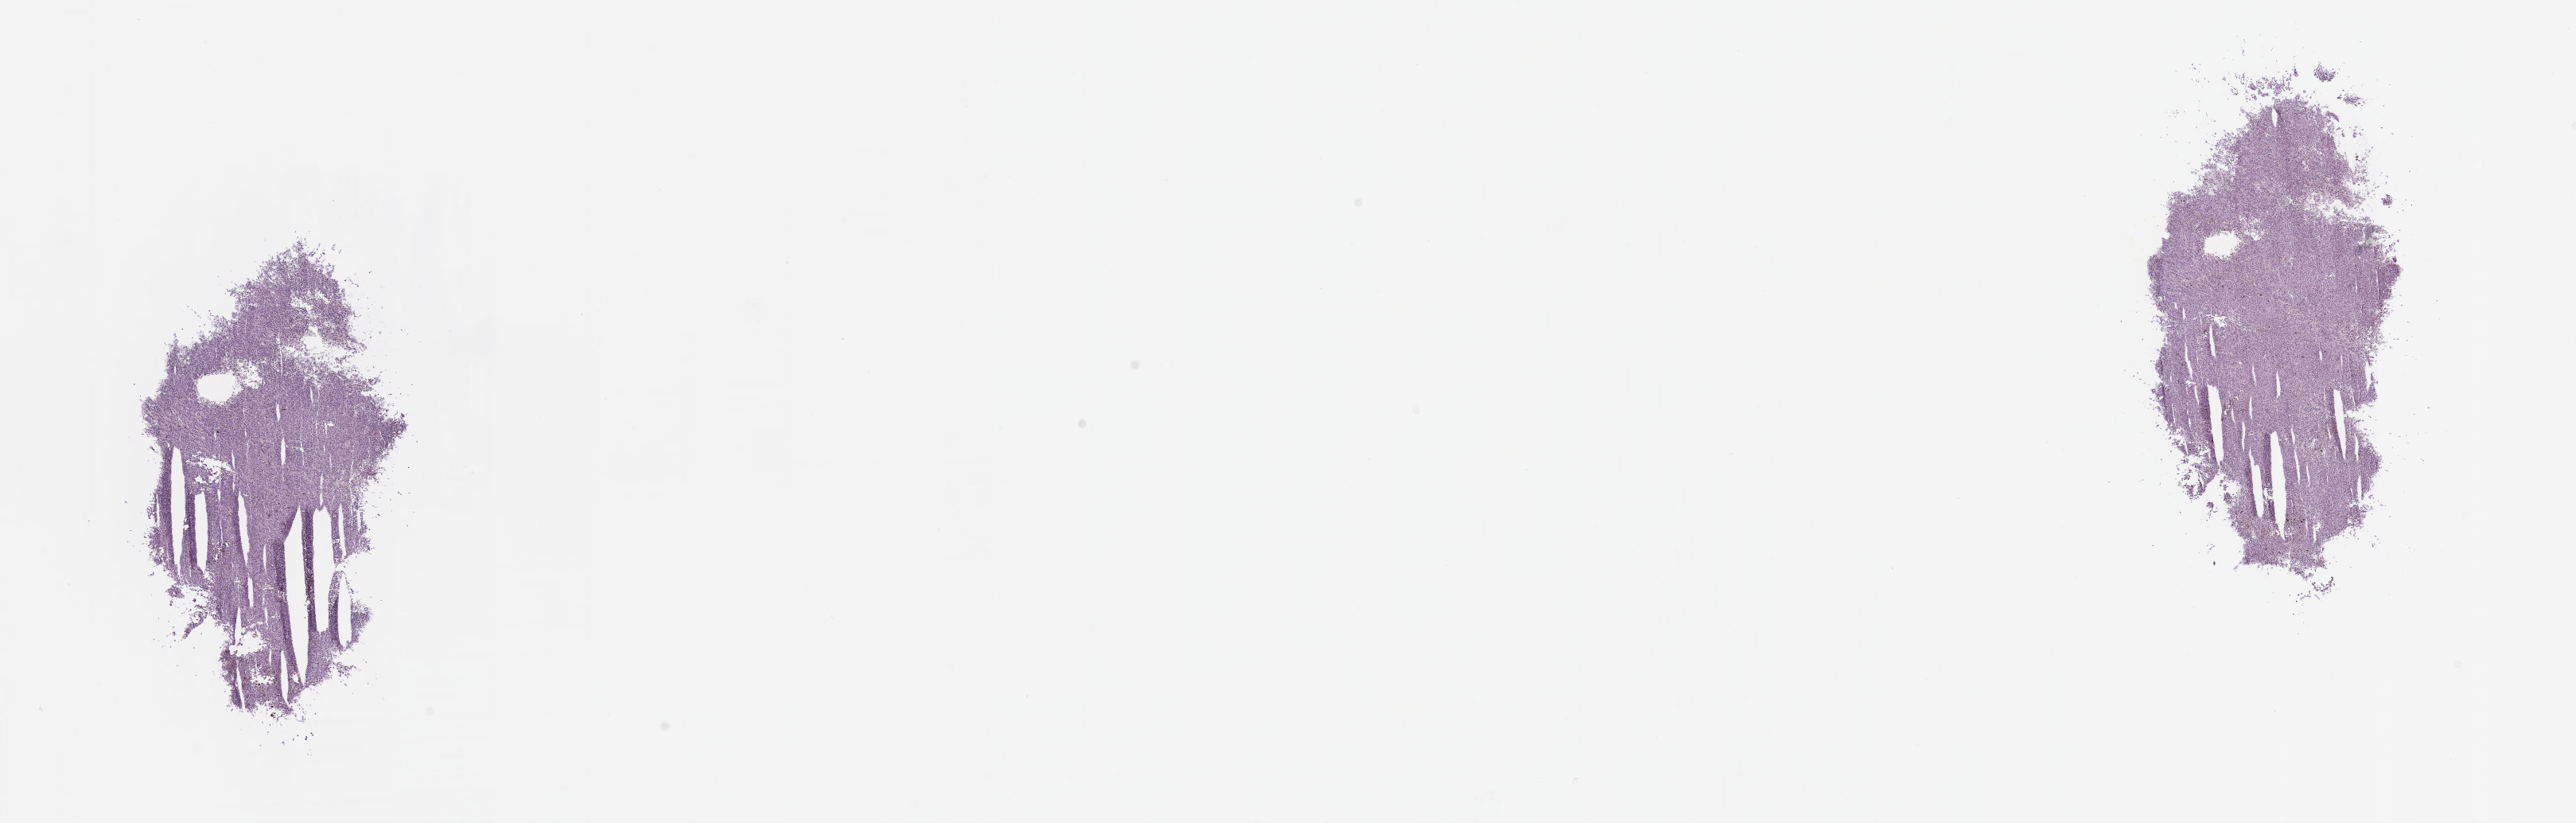
Digitized H&E tissue section (whole slide), whole scanned area (about 26.1 x 8.3 mm) shown as a low-resolution overview; frozen section from the top of the tissue portion; sample: primary tumour, uvea. Male patient; age at initial diagnosis 86 years. Slide review estimates, as recorded: tumour cells 90%, tumour nuclei 95%, normal cells 0%, stromal cells 10%, necrosis 0%. Infiltration values recorded for this section: lymphocyte infiltration 0%, monocyte infiltration 0%, neutrophil infiltration 0%.
- pathologic diagnosis: Epithelioid cell melanoma (choroid)
- AJCC pathologic stage: IIB
- TNM: T3a N0 M0